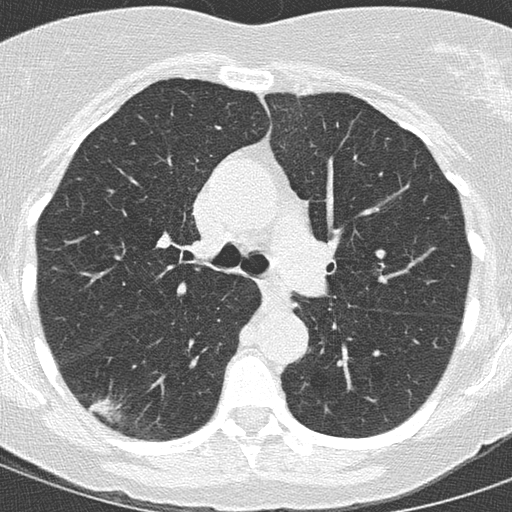
Axial slice from a low-dose chest CT screening exam; baseline screening round; lung window (W 1500 / L -600 HU); lung (sharp) reconstruction kernel (B50f). Female participant, aged 59 years at enrolment. Former smoker at enrolment.
Lesion marked by an expert reader, bounding box [x1, y1, x2, y2] px = [72, 384, 147, 441]. Screening reader's record for this exam (one nodule recorded; not confirmed to be the boxed lesion): non-calcified nodule or mass ≥4 mm, right lower lobe, 24 × 15 mm, spiculated (stellate) margins, soft tissue attenuation. Official screen result: positive, change unspecified: nodule(s) >= 4 mm or enlarging nodule(s), mass(es), or other non-specific abnormalities suspicious for lung cancer. Lung cancer was diagnosed 12 days after this screen: adenocarcinoma, NOS, right lower lobe, moderately differentiated (G2), stage IIB (AJCC 6th edition), 22 mm at pathology.